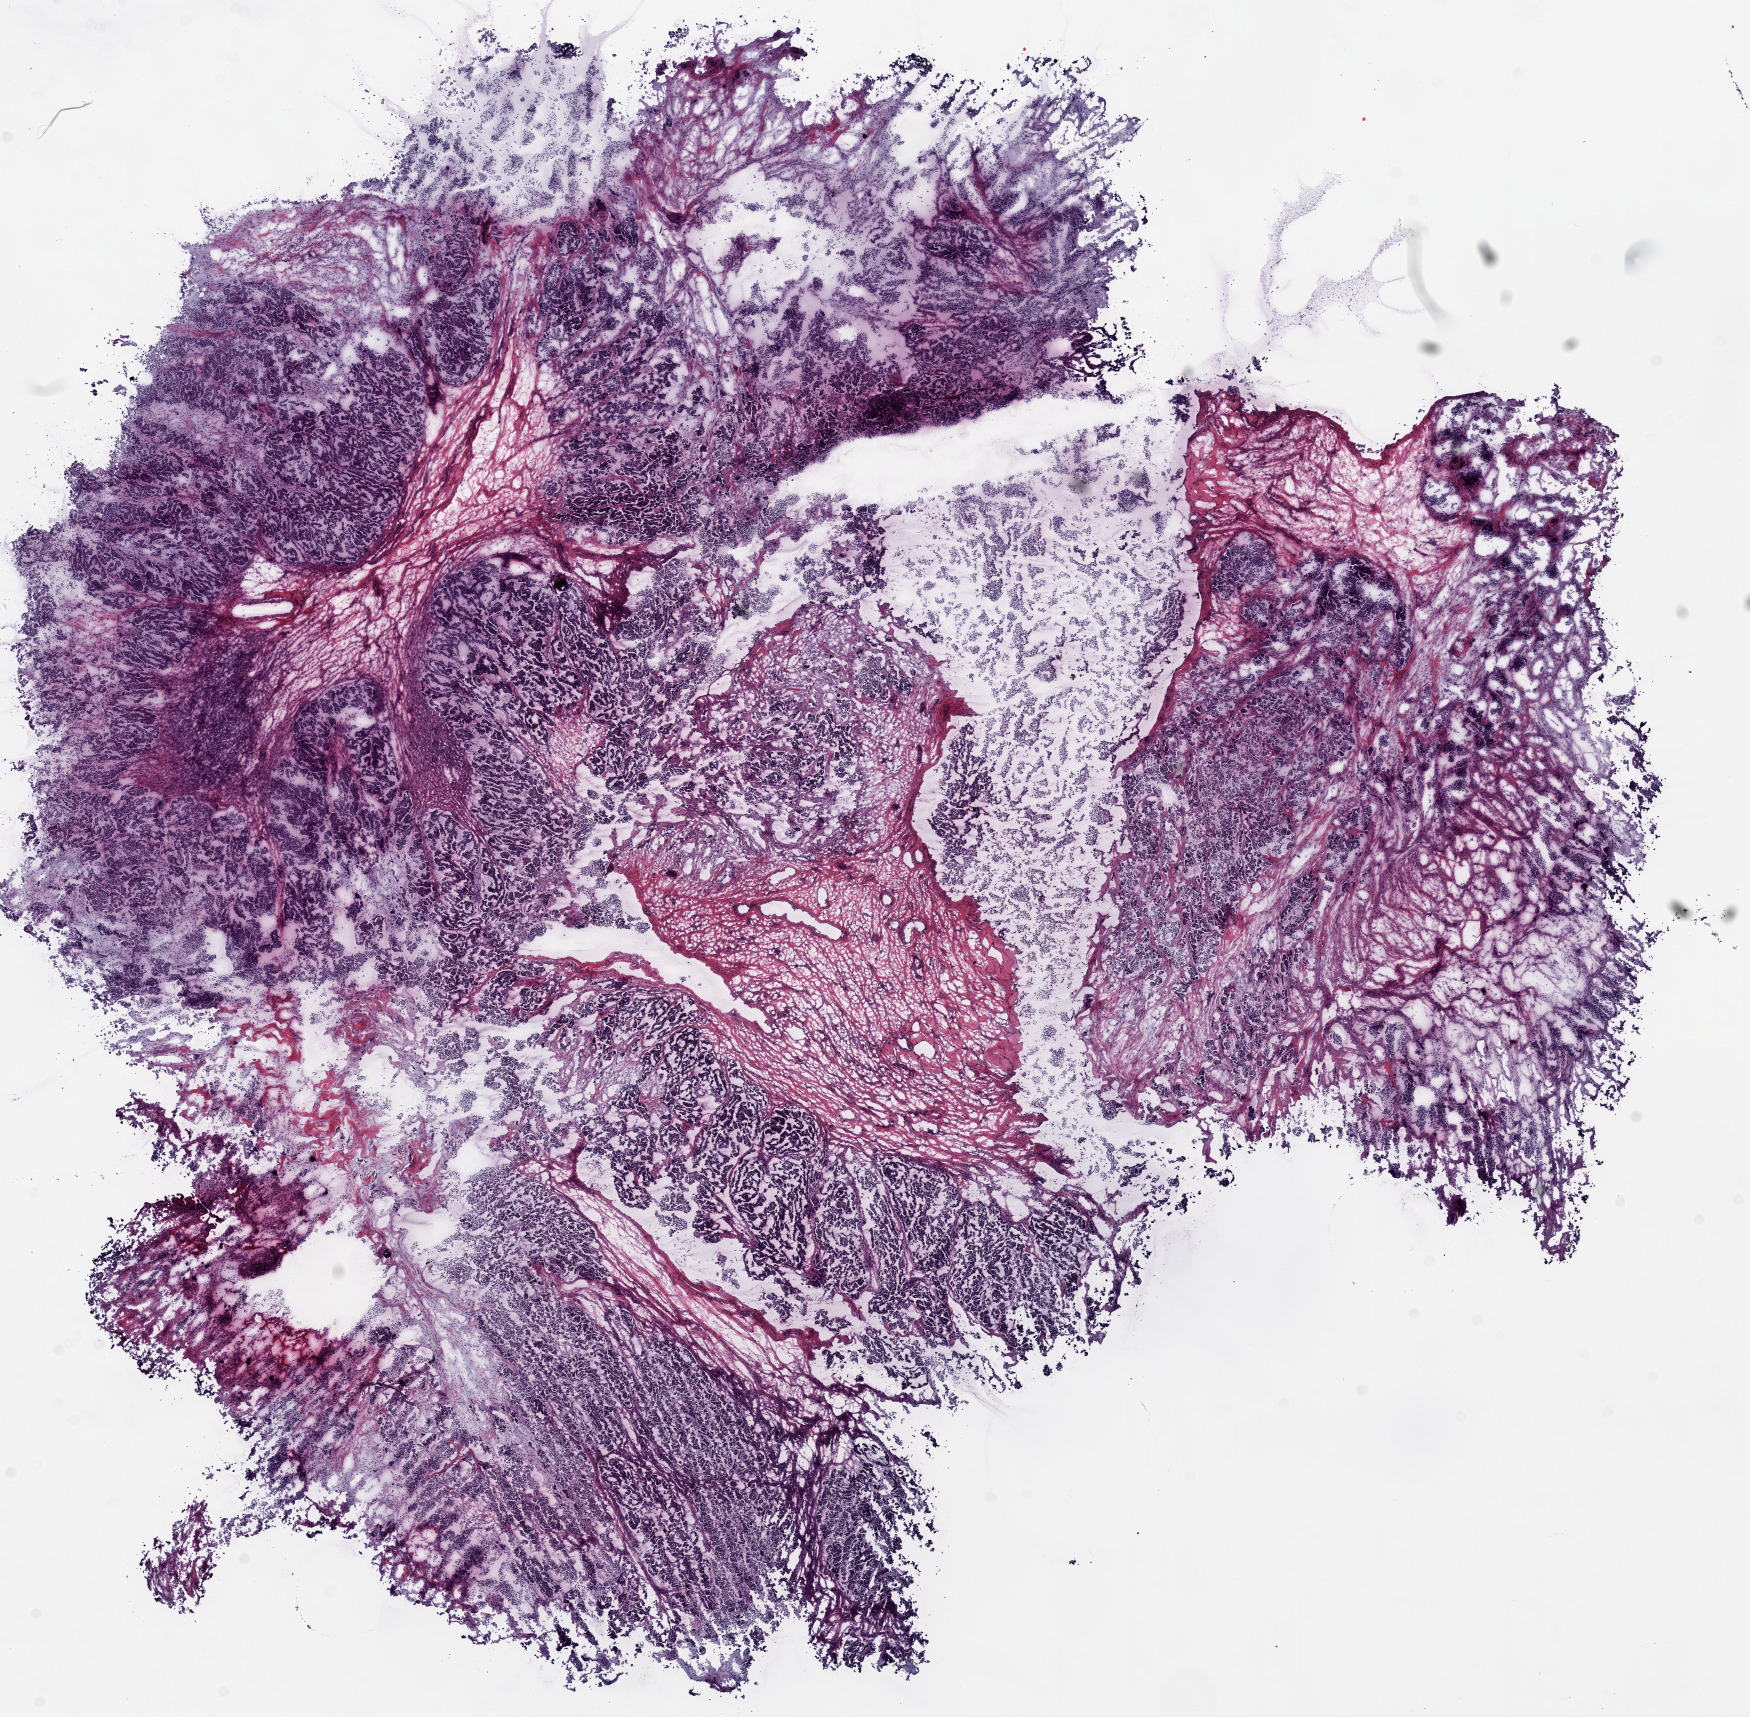
Digitized H&E tissue section (whole slide) — low-resolution overview of the scanned area, about 14.0 x 13.8 mm (slide scanned at 20x); frozen section from the top of the tissue portion; ovary, primary tumour sample. Female patient; age at initial diagnosis 49 years. Histologic grade: G2 (moderately differentiated). Pathologist review of this section (percent, as recorded): tumour cells 80%, tumour nuclei 80%, normal cells 0%, stromal cells 15%, necrosis 5%.
* FIGO stage: IV
* pathologic diagnosis: Serous cystadenocarcinoma, NOS